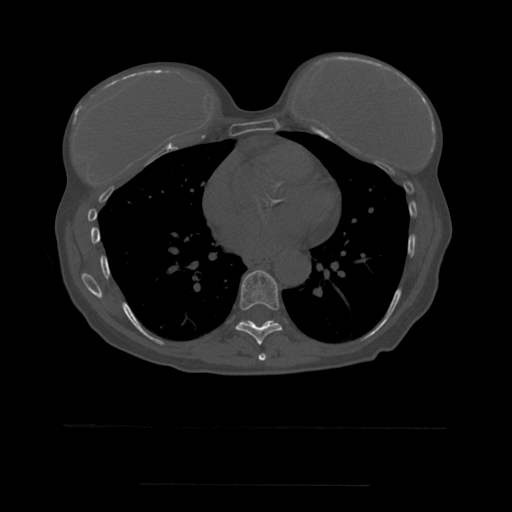
CT including the spine, one axial slice. Slice 337 of 544 in the series (ordered by position). Bone window (W 1800 / L 400 HU). 1.25 mm slice thickness. 512 × 512 image matrix, field of view 350 × 350 mm. Patient age 58 years. Case-level facts recorded for this patient, not image findings: primary cancer: lung.
Outlined on this slice (semi-automatic segmentation, software-assisted and operator-edited):
- T7 vertebra: bounding box [x1, y1, x2, y2] px = [258, 354, 267, 361]
- T8 vertebra: [236, 270, 283, 345]